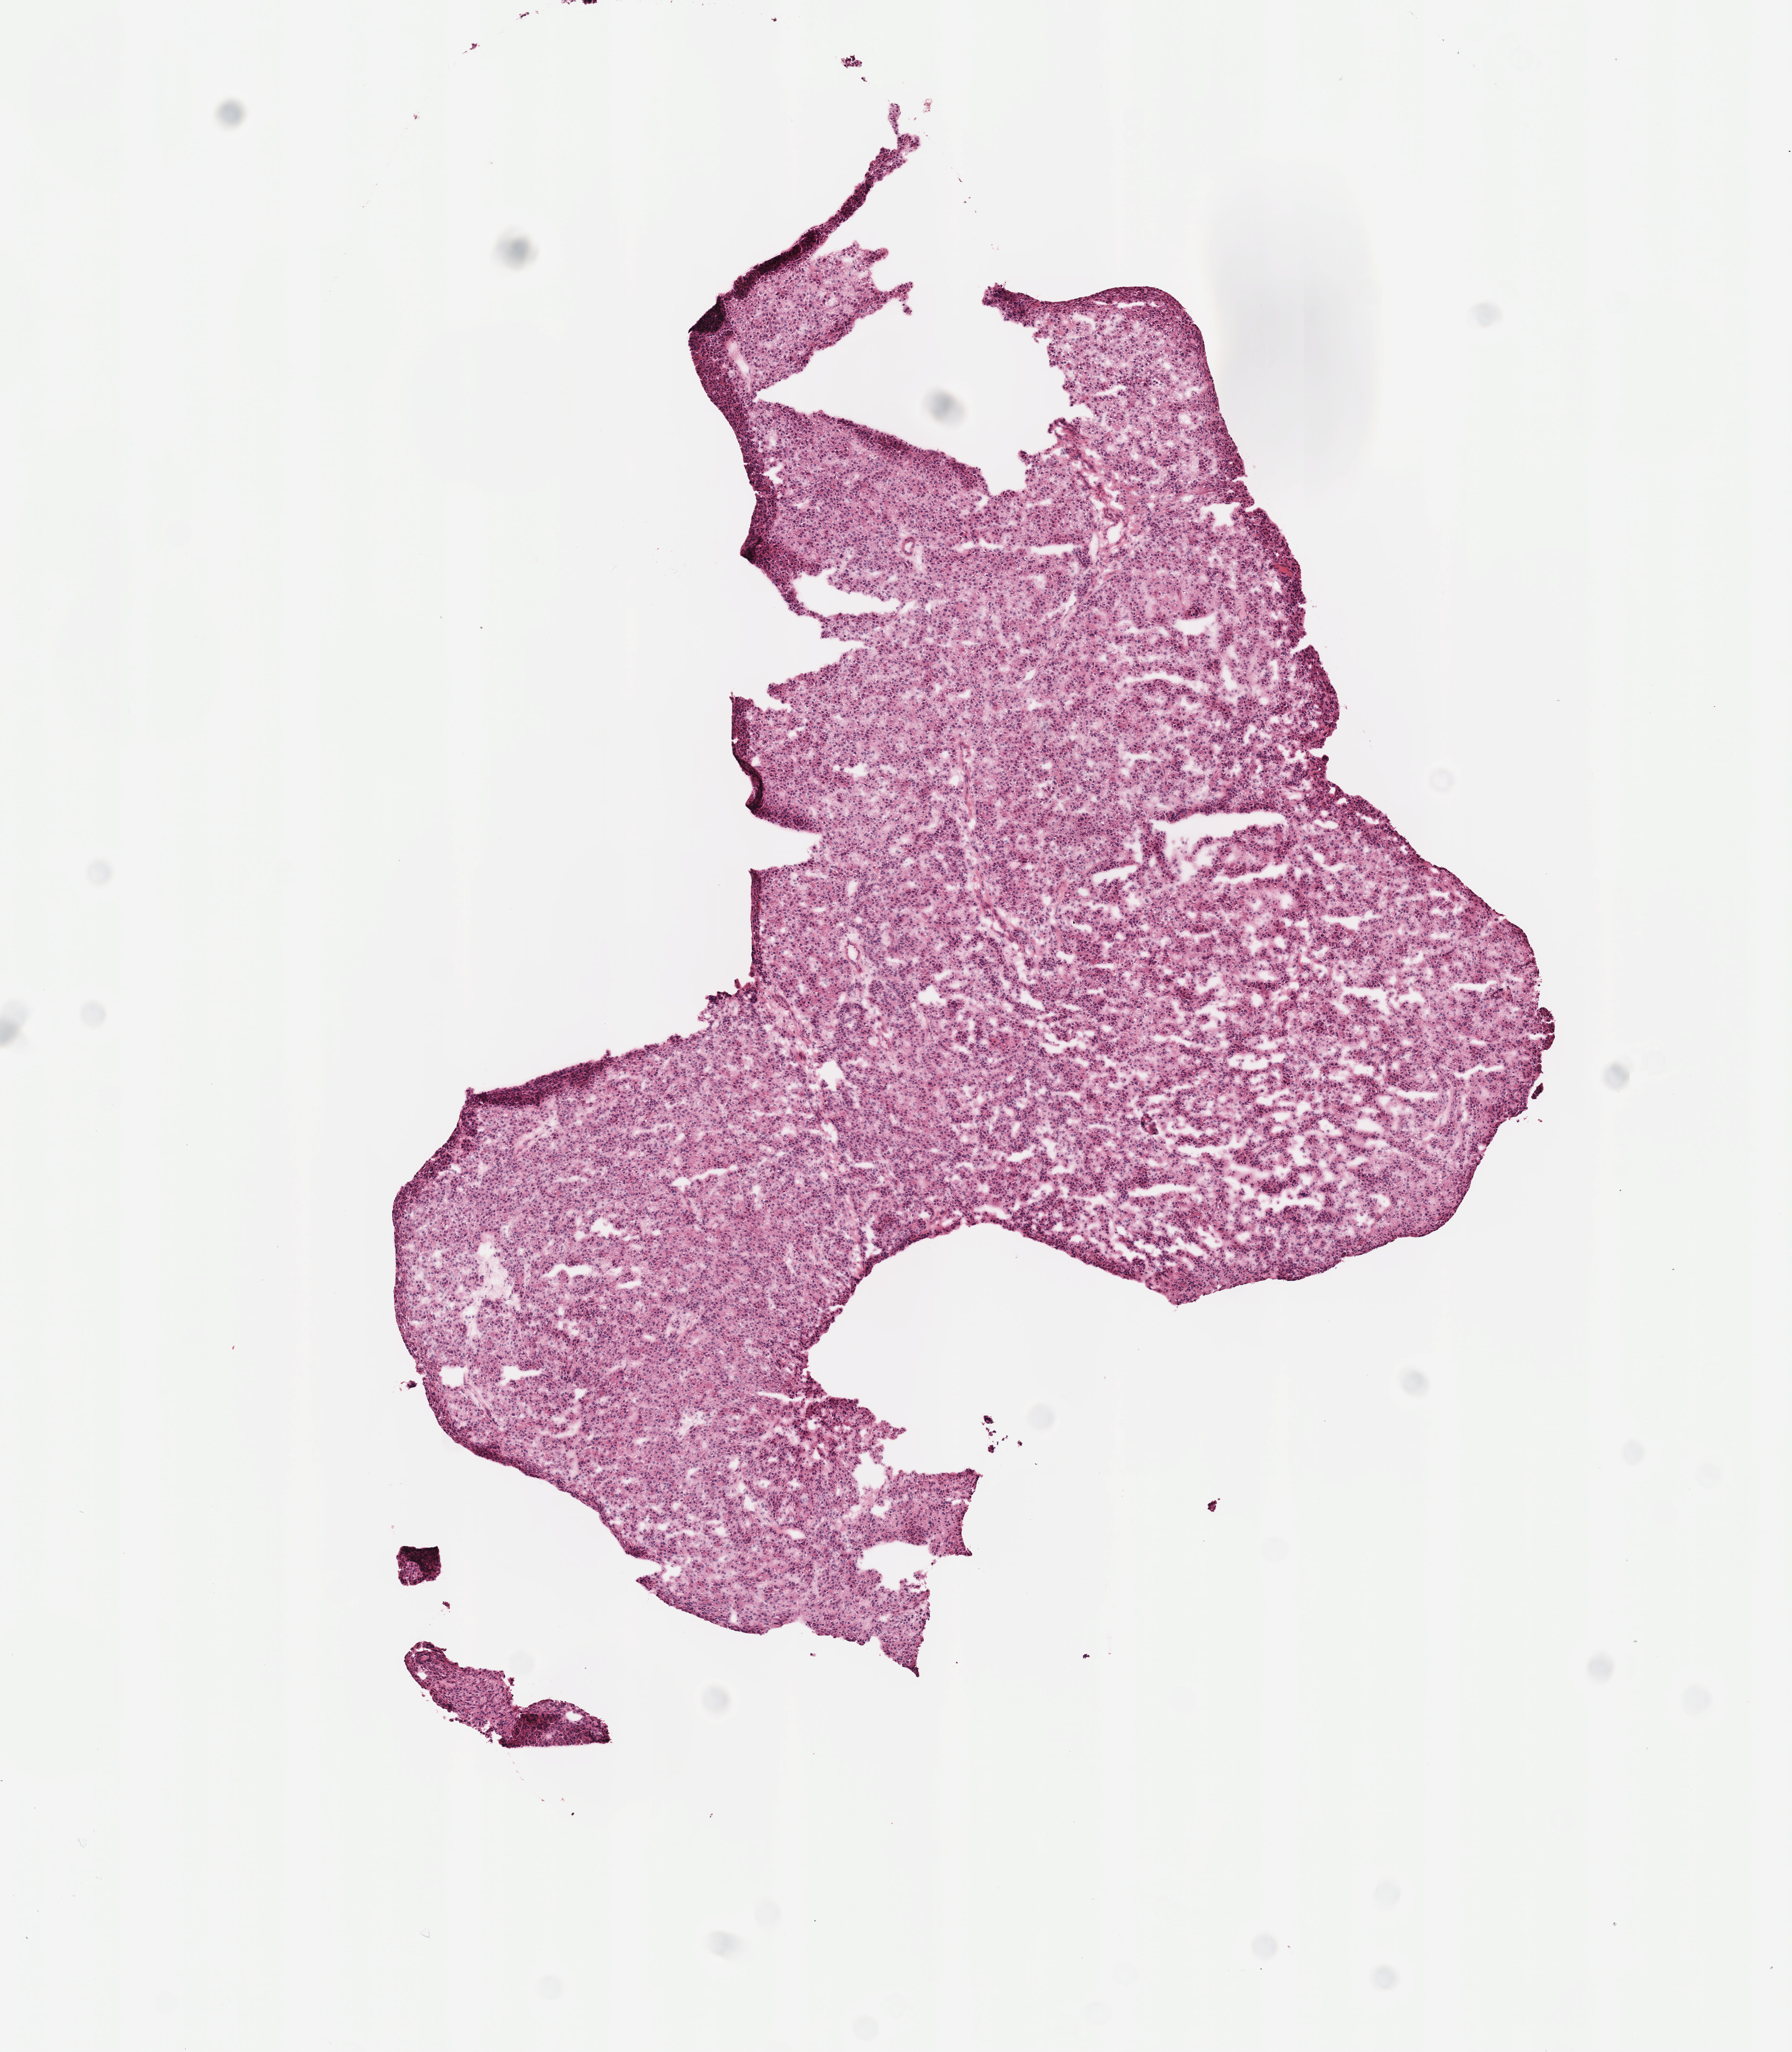
Whole-slide histology image, Hematoxylin and eosin (H&E) stained — shown as a low-resolution overview of the whole scanned area (about 5.5 x 6.3 mm), frozen section, sample: primary tumour, liver. Female patient; age at initial diagnosis 55 years. Histologic grade: G2 (moderately differentiated). Slide review estimates, as recorded: tumour cells 100%, tumour nuclei 80%, normal cells 0%, stromal cells 0%, necrosis 0%. Inflammatory infiltration, as recorded: lymphocyte infiltration 1%, monocyte infiltration 0%, neutrophil infiltration 0%.
AJCC pathologic stage: I (7th edition). Histologic diagnosis: Hepatocellular carcinoma, NOS.